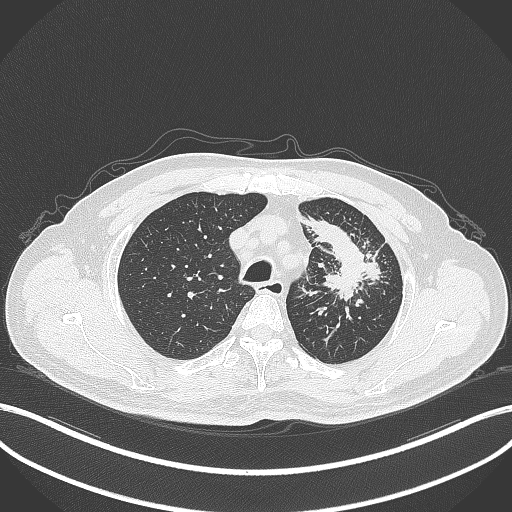
Chest CT, one axial slice; position 281 of 386 along the scan axis; reconstruction kernel B70f; lung window (W 1500 / L -600 HU); 512 × 512 image matrix, field of view 400 × 400 mm. Male patient, age 69 years. From the clinical record (not read from this slice): clinical TNM (as recorded): T2a N2 M0; histopathological grade: G2-3.
Outlined on this slice (rectangle marked by the reading radiologist):
- lung tumour (recorded histology: adenocarcinoma): bounding box (x1, y1, x2, y2) in pixels: (298, 211, 389, 300)